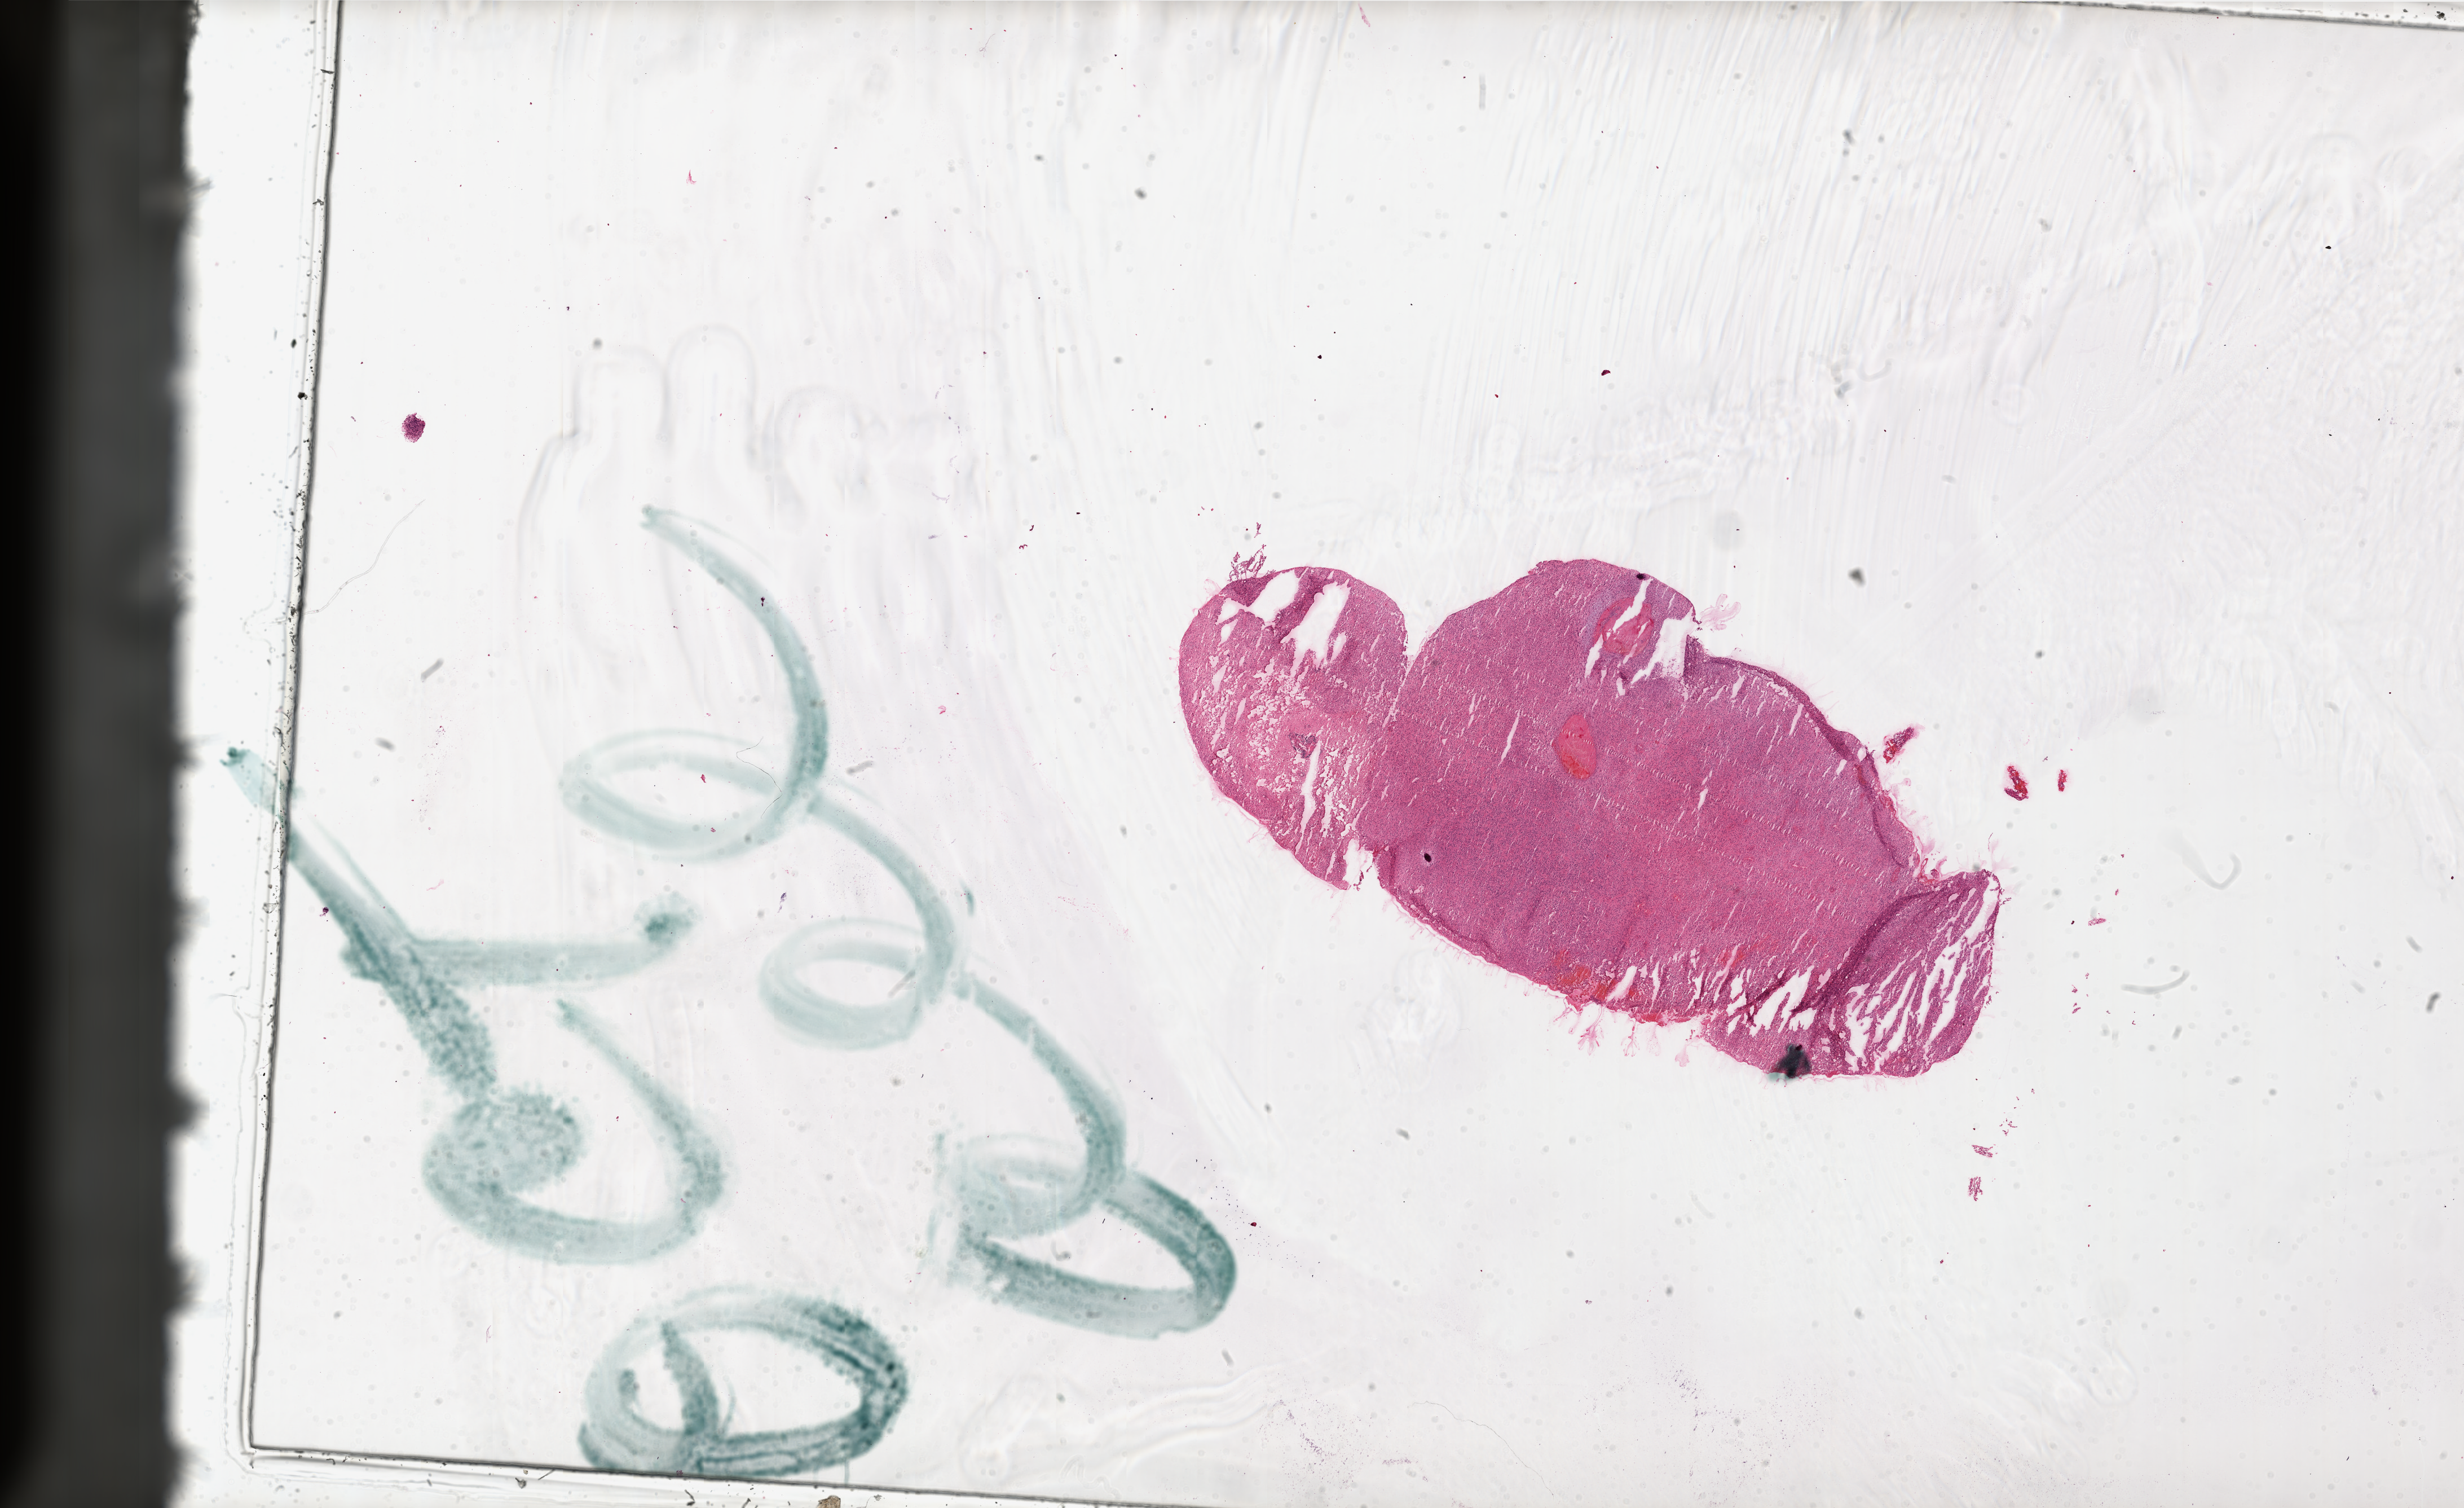
Whole-slide histology image, H&E, low-resolution overview of the scanned area, about 35.0 x 21.4 mm (acquisition: 20x scan). Frozen section. Brain, primary tumour sample. Patient: male, age at initial diagnosis 63 years. Composition of this section per pathologist review: tumour cells 90%, tumour nuclei 100%, normal cells 0%, stromal cells 0%, necrosis 10%. Infiltration values recorded for this section: lymphocyte infiltration 100%, monocyte infiltration 0%, neutrophil infiltration 0%.
Histologic diagnosis: Glioblastoma.